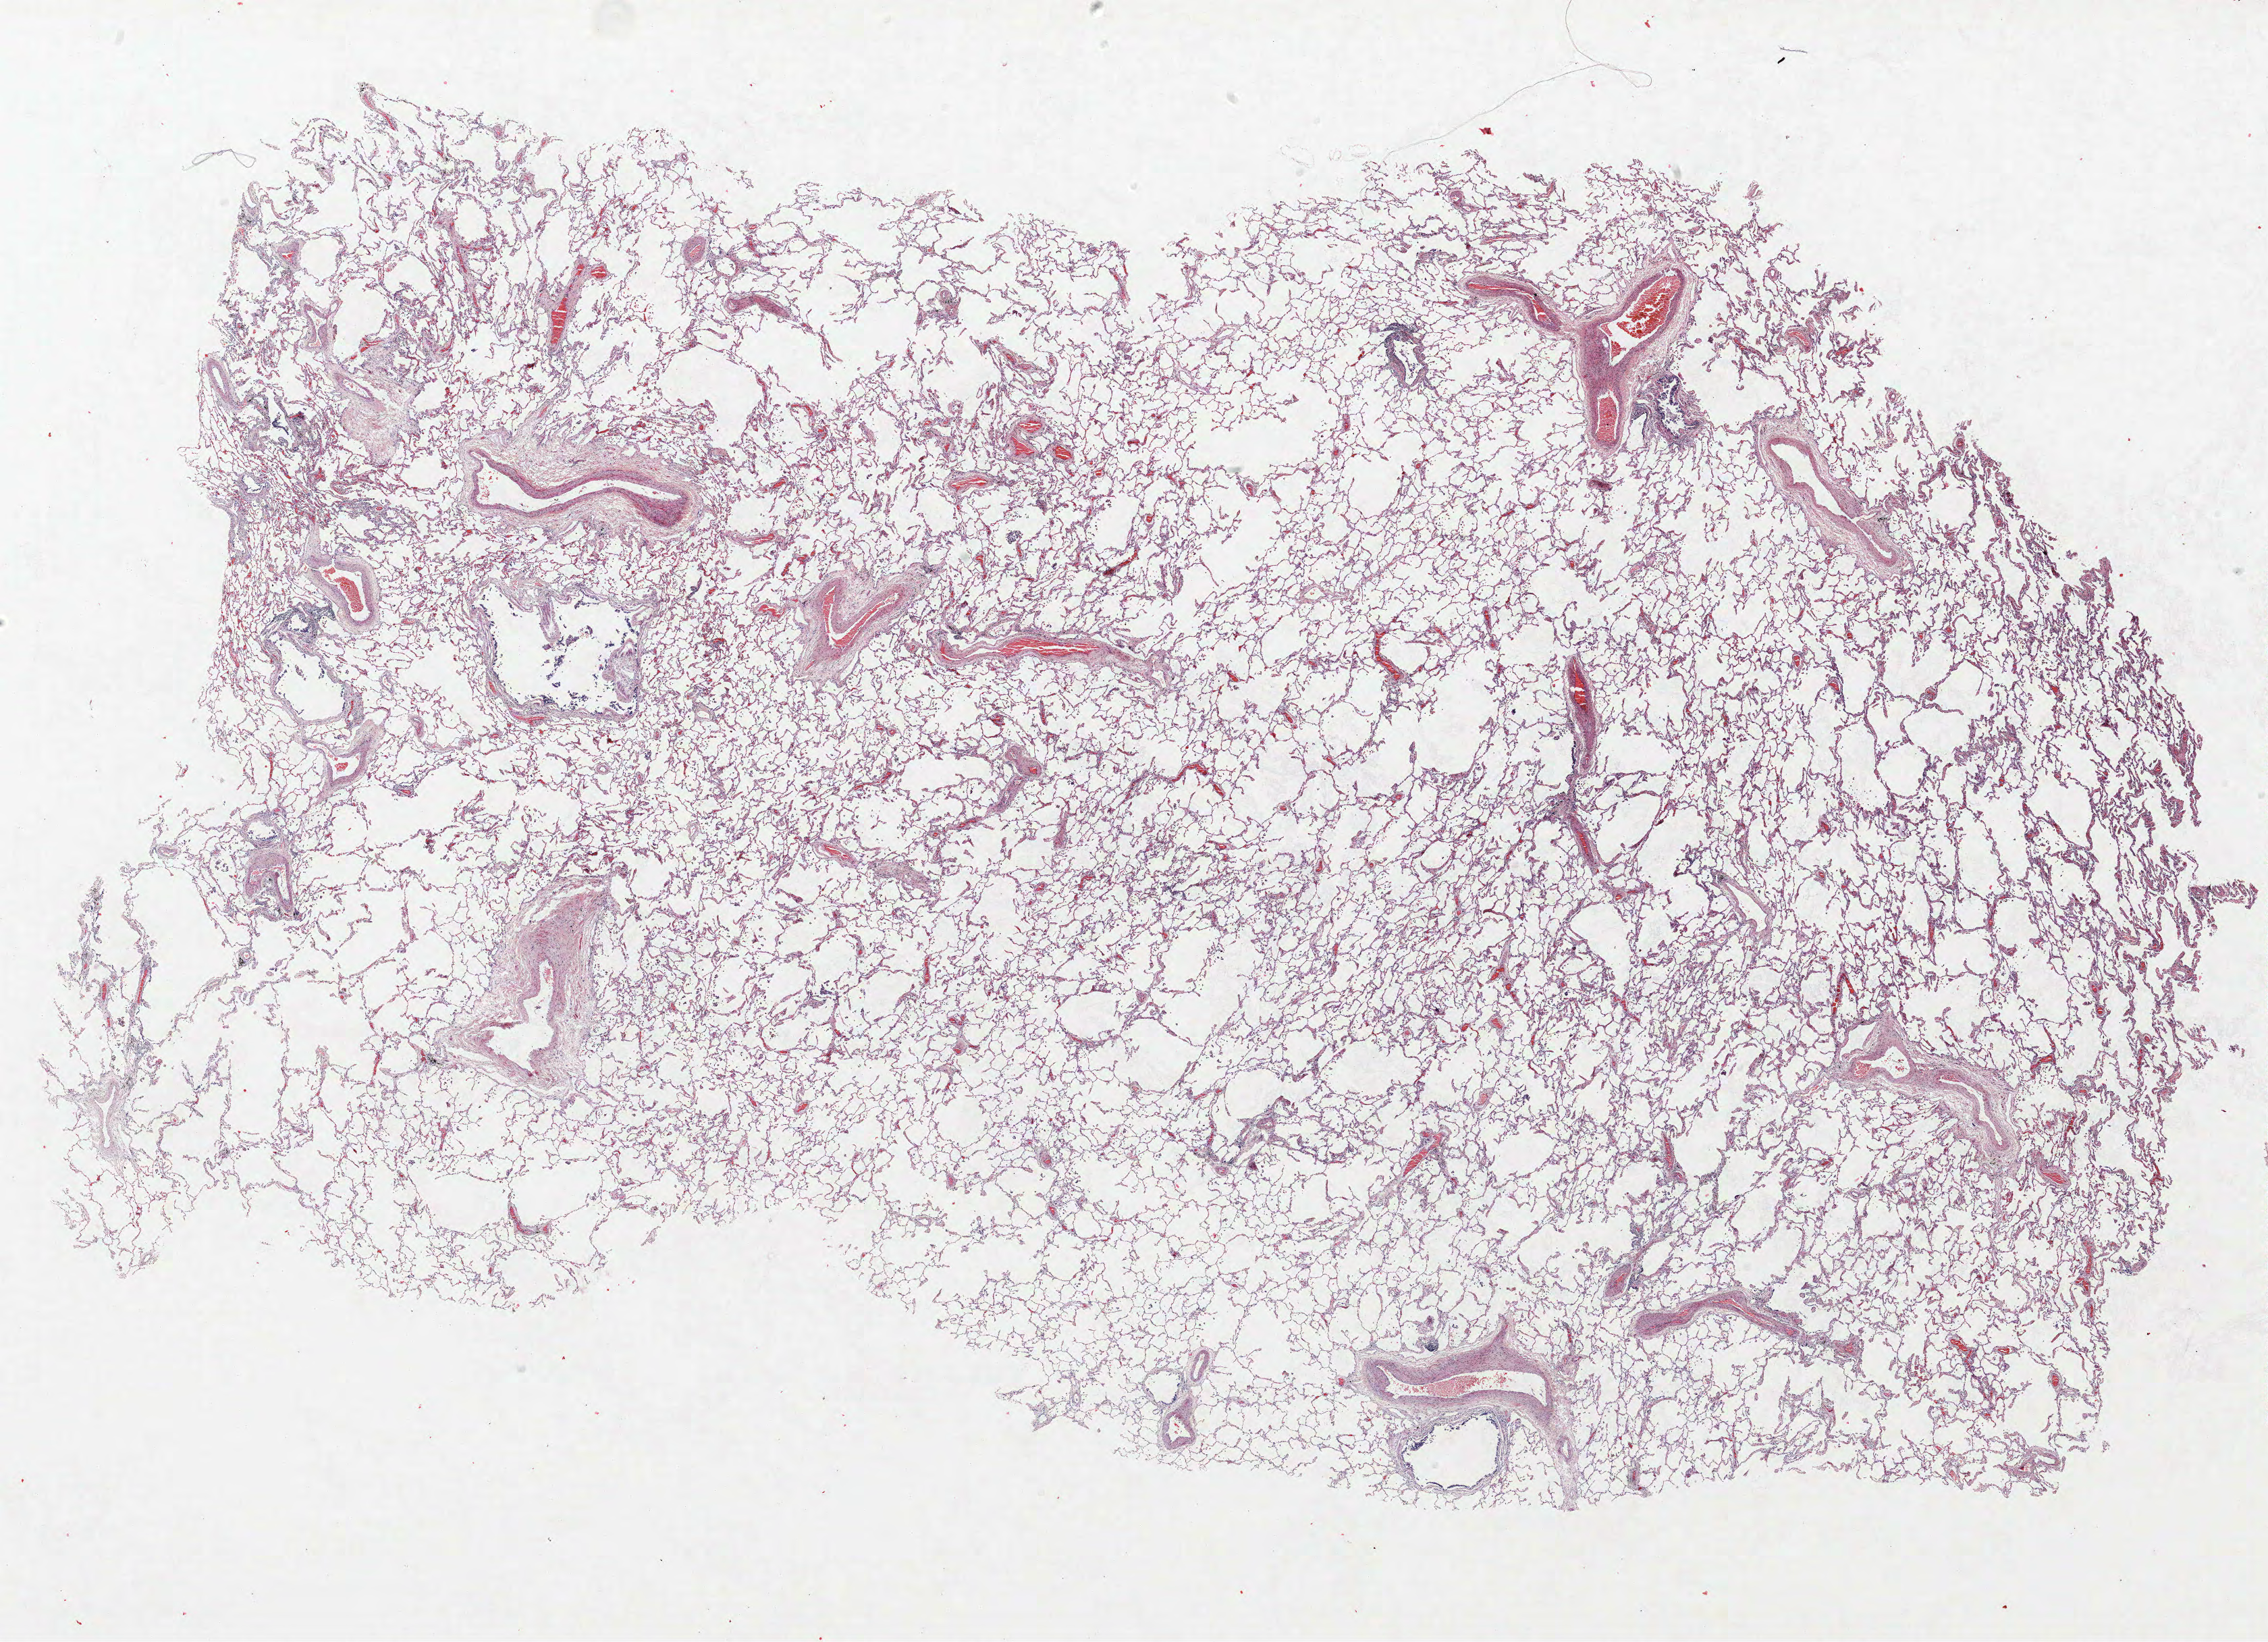
H&E whole-slide image, whole scanned area (about 26.9 x 19.5 mm, slide scanned at 40x) shown as a low-resolution overview. FFPE section. Lung. Female, age 55 at enrolment. Current smoker at enrolment.
Participant's lung-cancer diagnosis: Adenocarcinoma, NOS.